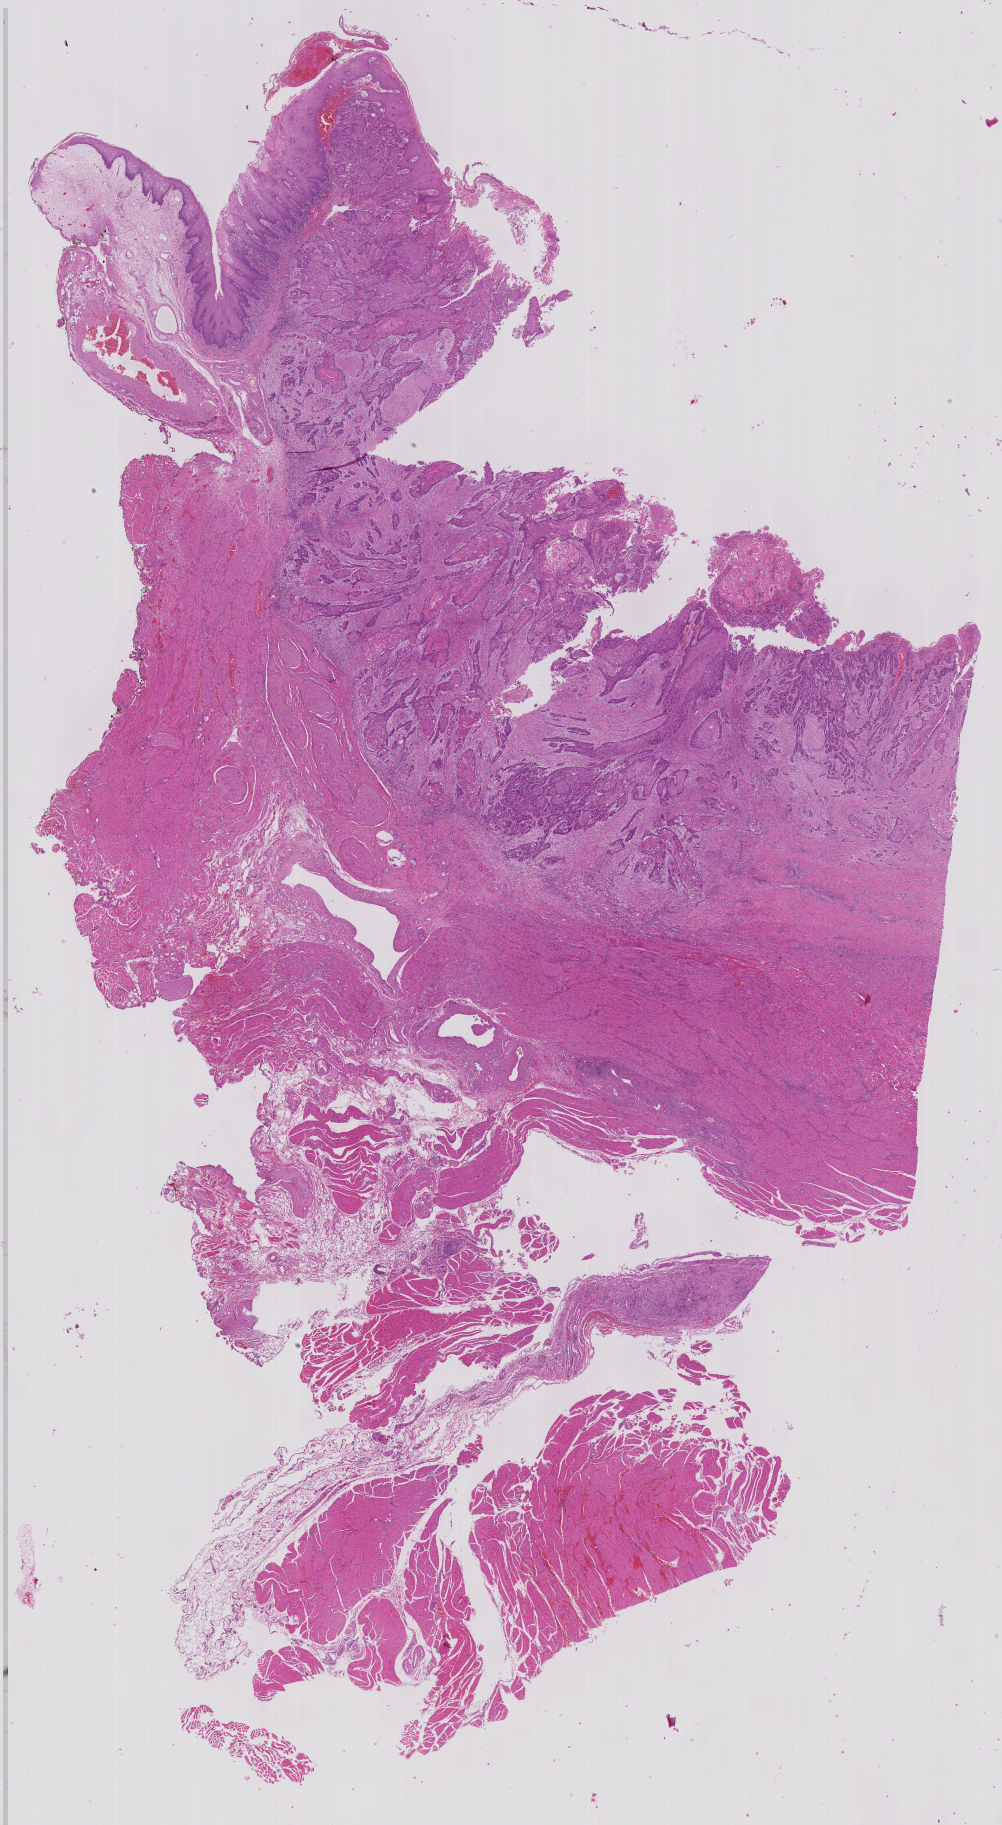
H&E whole-slide image — low-resolution overview of the scanned area, about 16.0 x 29.2 mm (from a 40x scan). Formalin-fixed paraffin-embedded (FFPE) diagnostic section. Head and neck, primary tumour sample. Male patient; age at initial diagnosis 58 years. Histologic grade: G2 (moderately differentiated).
* diagnosis: Squamous cell carcinoma, keratinizing, NOS (floor of mouth, NOS)